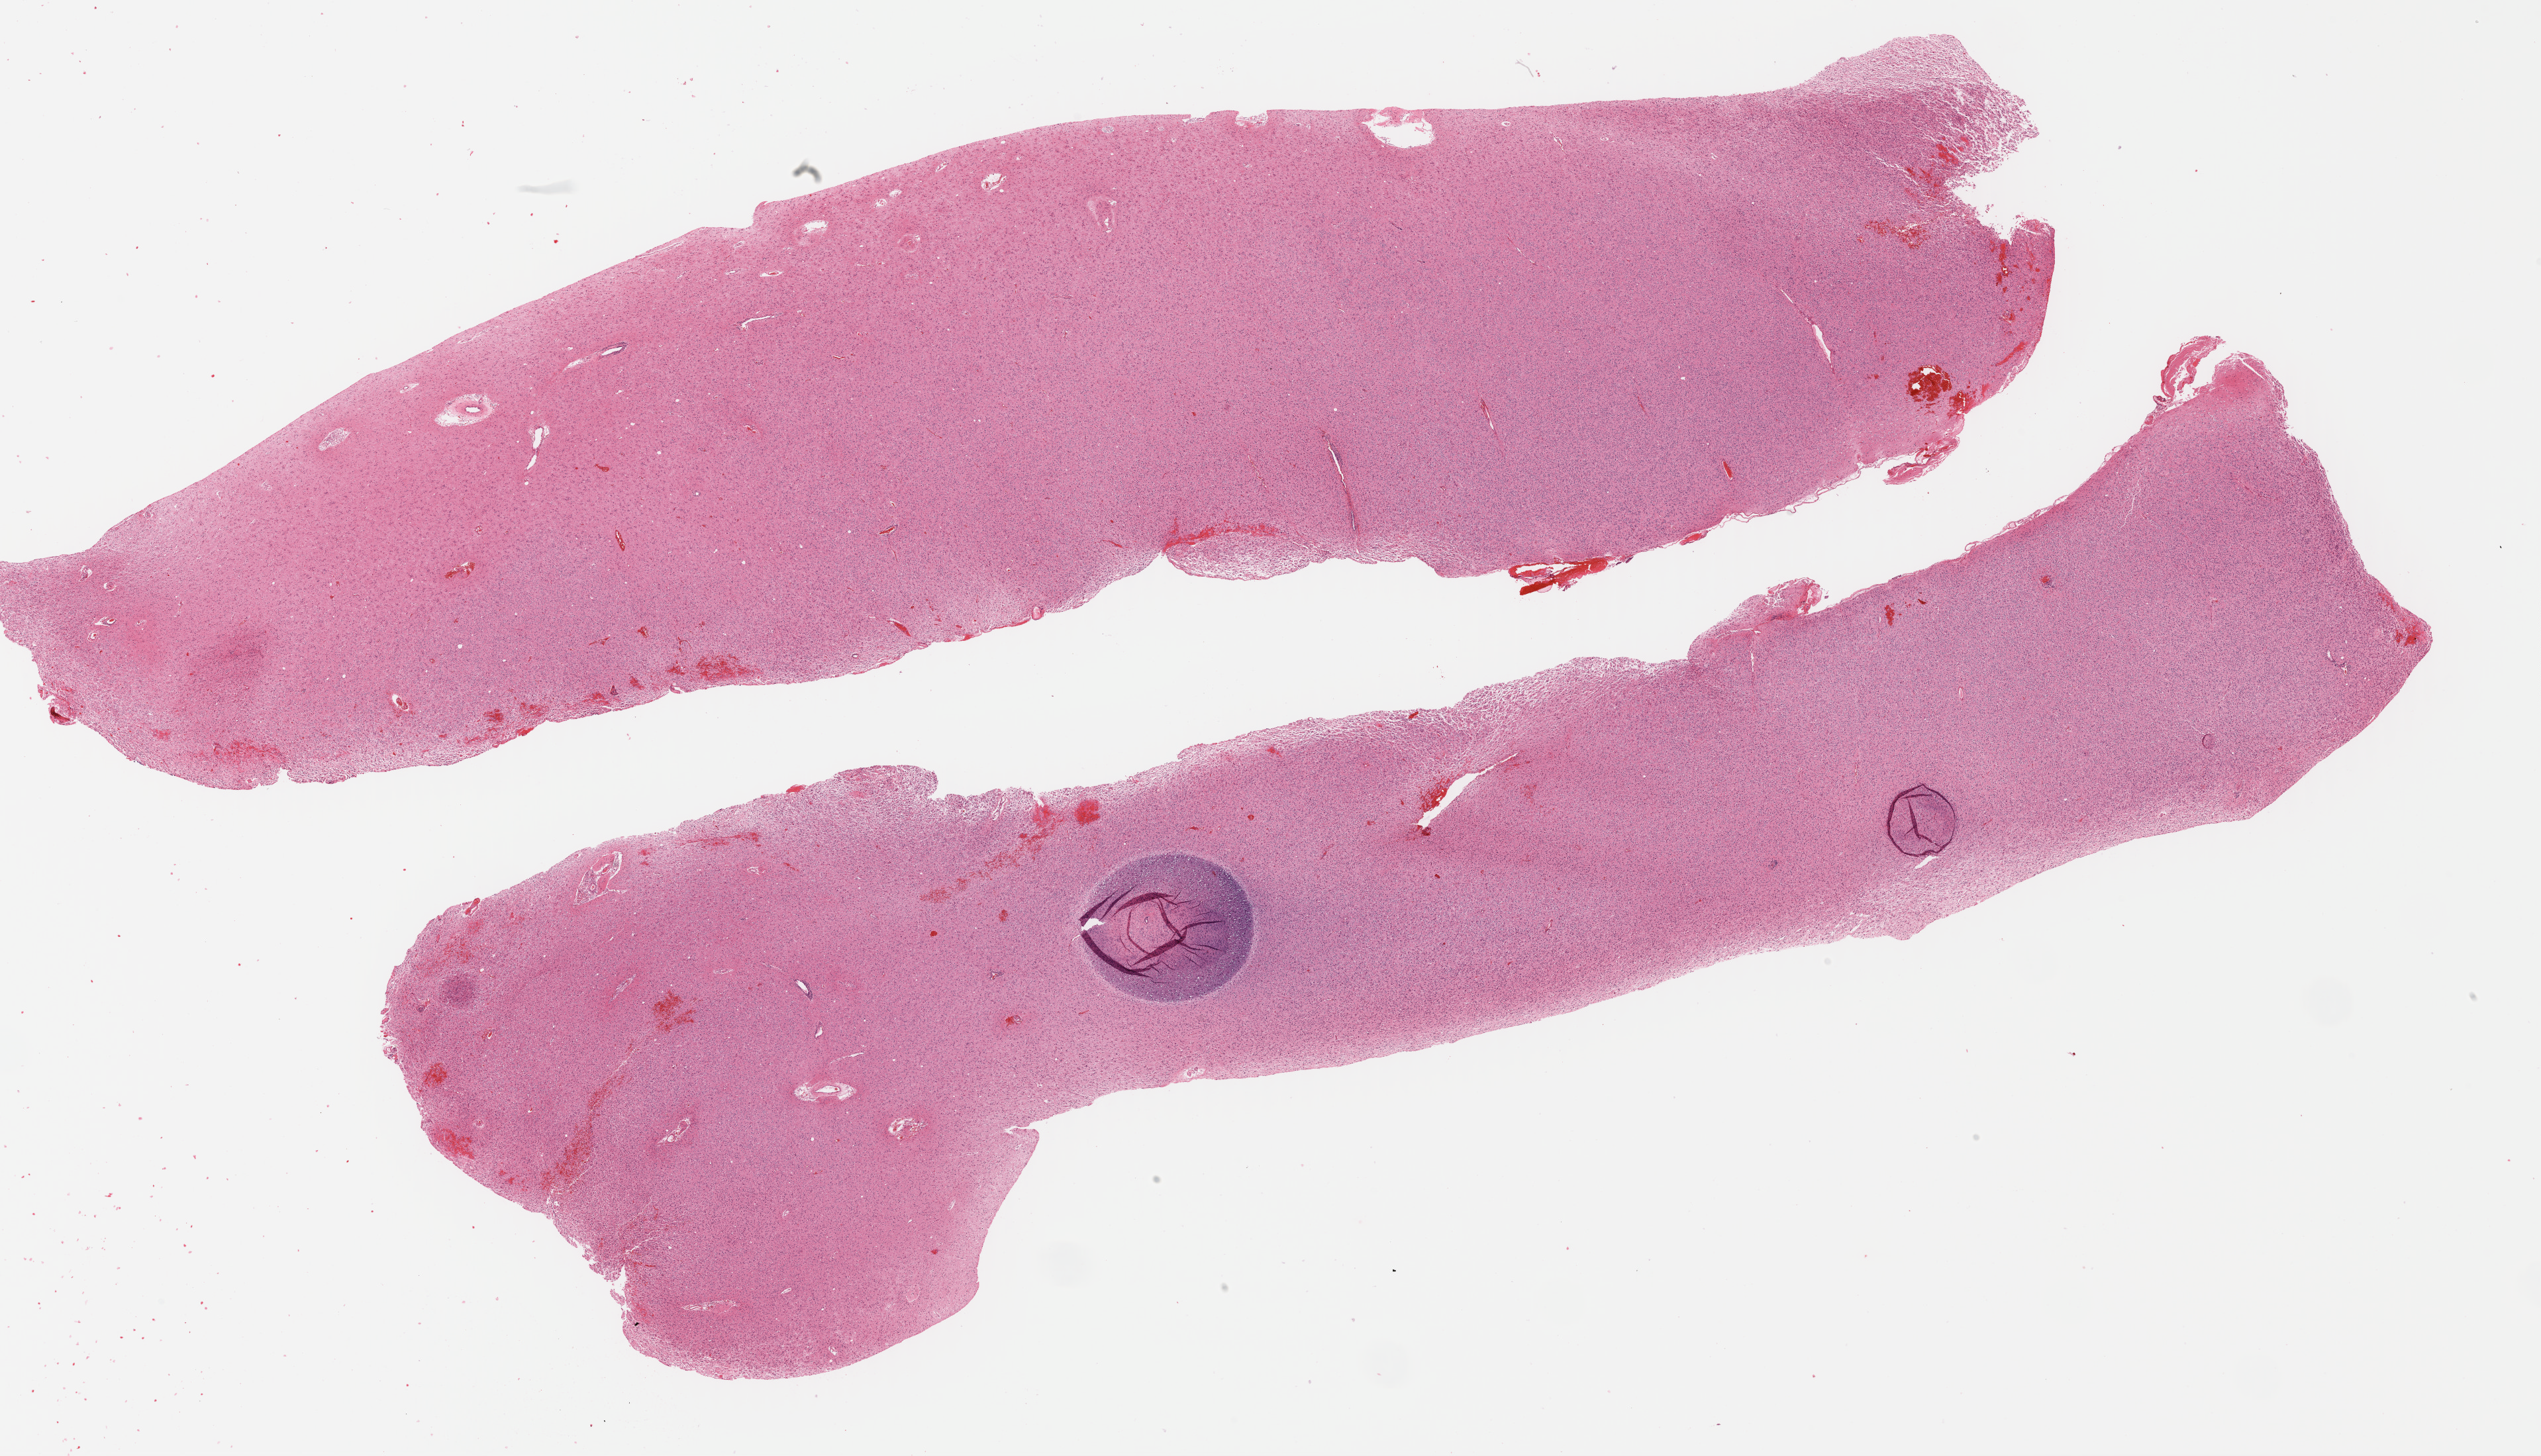
Digitized Hematoxylin and eosin (H&E) stained tissue section (whole slide), a low-resolution overview of the entire scanned area, about 30.2 x 17.3 mm. Formalin-fixed paraffin-embedded (FFPE) diagnostic section. Brain, primary tumour sample. Female patient; age at initial diagnosis 47 years. Histologic grade: G2 (moderately differentiated).
Laterality: left. Pathologic diagnosis: Mixed glioma.